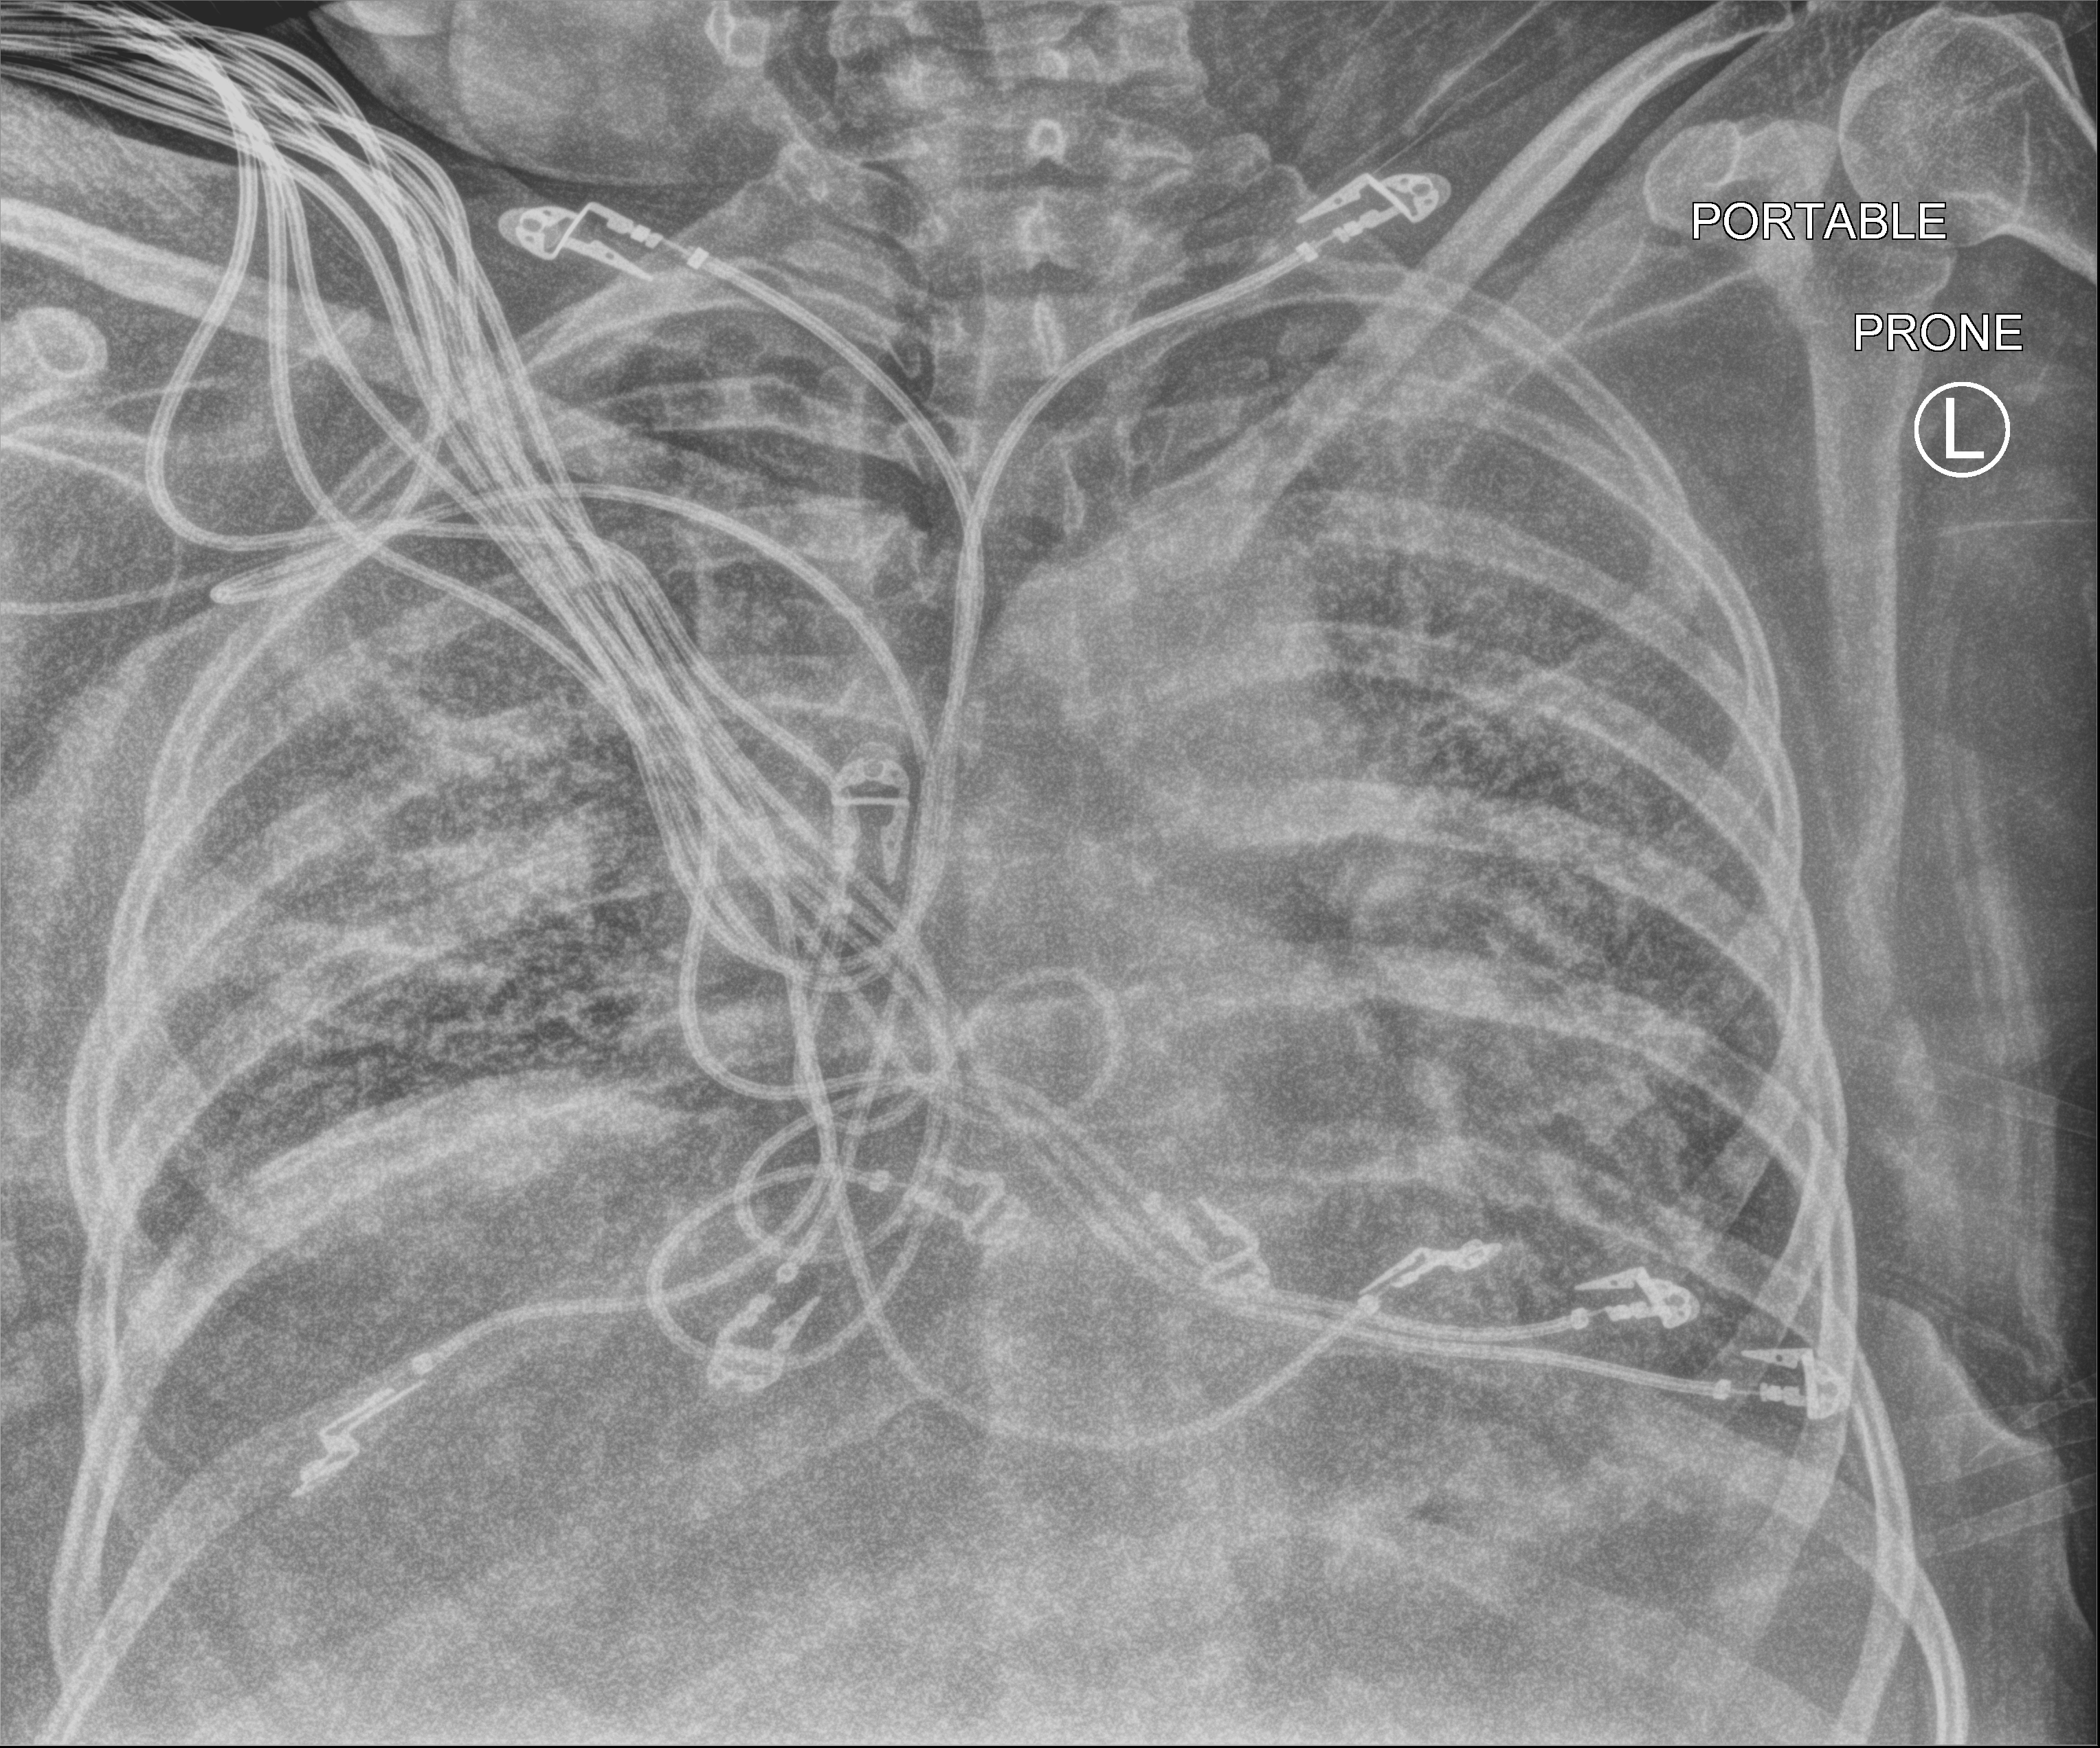
Portable chest radiograph; anteroposterior (AP) projection. Female patient hospitalised with COVID-19, age 18–59 years.
Admission-level facts for this patient (not findings on this image; timing relative to this image not recorded): admitted to intensive care during this hospital stay: yes; chronic kidney disease (admission record): no.